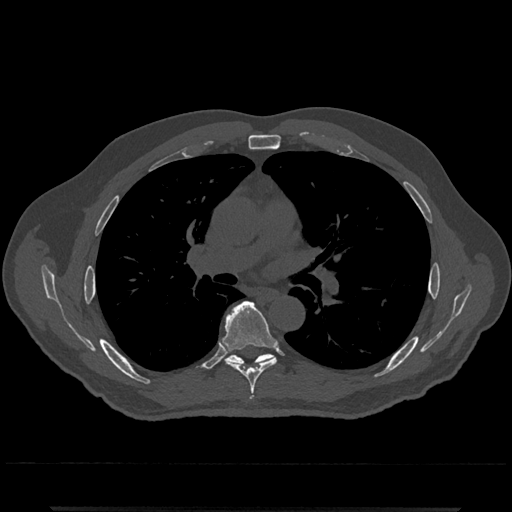
CT including the spine, one axial slice; position 757 of 797 along the scan axis; reconstruction kernel Br40s/3; 120 kVp; bone window (W 1800 / L 400 HU); 0.5 mm slice thickness; 512 × 512 image matrix, field of view 393 × 393 mm. Patient: male, 67 years. Case-level facts recorded for this patient, not image findings: primary cancer: prostate.
Structures marked on this image (semi-automatically segmented with operator editing):
- T6 vertebra: bounding box [x1, y1, x2, y2] px = [223, 301, 276, 400]
- T7 vertebra: [227, 353, 273, 365]